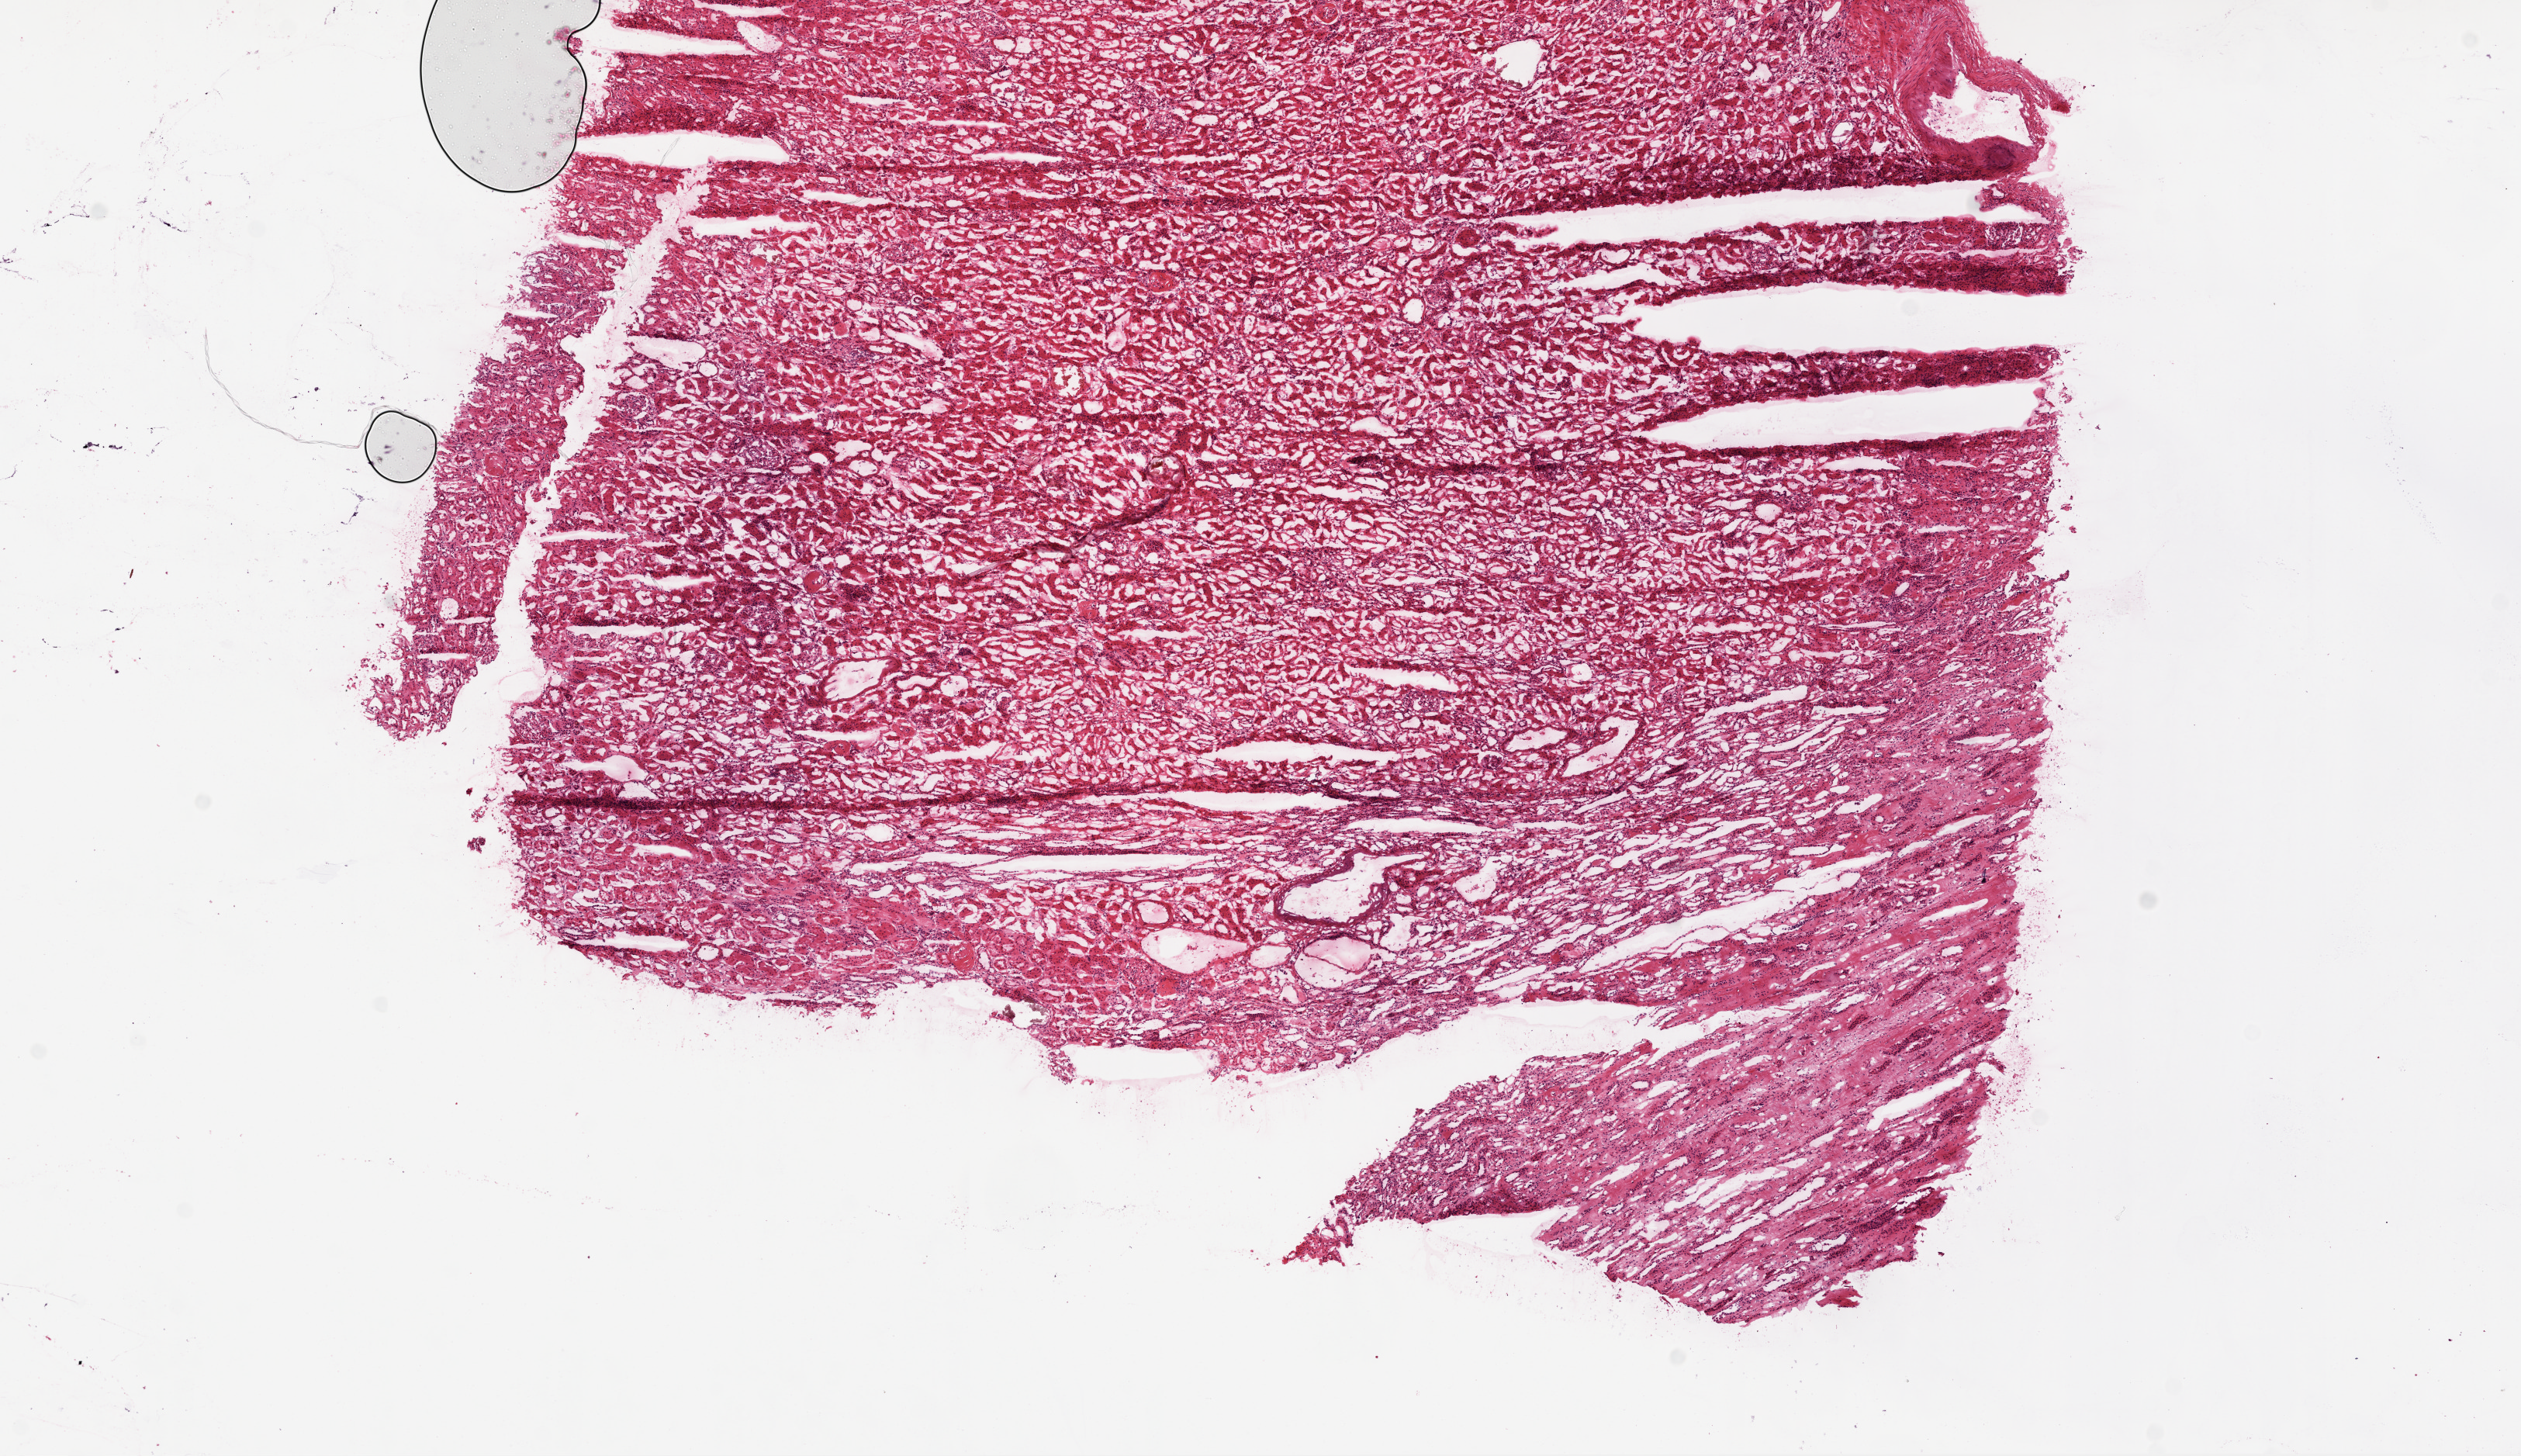
H&E whole-slide image — low-resolution overview of the scanned area, about 13.0 x 7.5 mm (from a 20x scan); frozen section; solid tissue normal (non-tumour tissue) sample from the kidney. Patient: female, age at initial diagnosis 75 years.
* this section: solid tissue normal sample (biorepository sample class)
* patient diagnosis: Clear cell adenocarcinoma, NOS